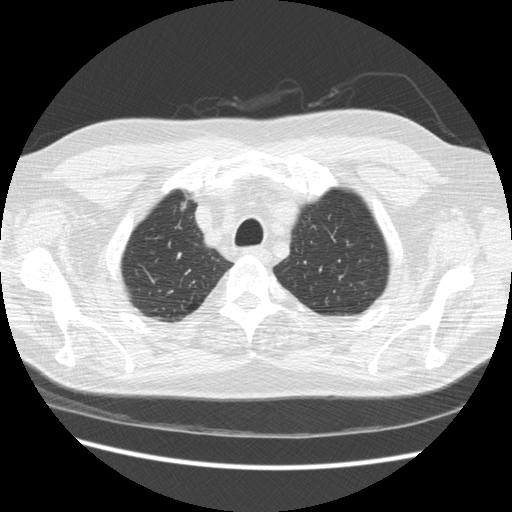
Axial slice from a low-dose chest CT screening exam; third screening round (two years after baseline); lung window (W 1500 / L -600 HU); standard (soft-tissue) reconstruction kernel (STANDARD); 512 × 512 image matrix. Male participant, aged 66 years at enrolment. Former smoker at enrolment.
Lesion marked by an expert reader, box from (x=168, y=189) to (x=206, y=221) px. Screening reader's record for this exam: no non-calcified nodule ≥4 mm recorded. Official screen result: positive, other. Lung cancer was diagnosed 229 days after this screen: bronchiolo-alveolar adenocarcinoma, NOS, right upper lobe, moderately differentiated (G2), stage IA (AJCC 6th edition), 12 mm at pathology.